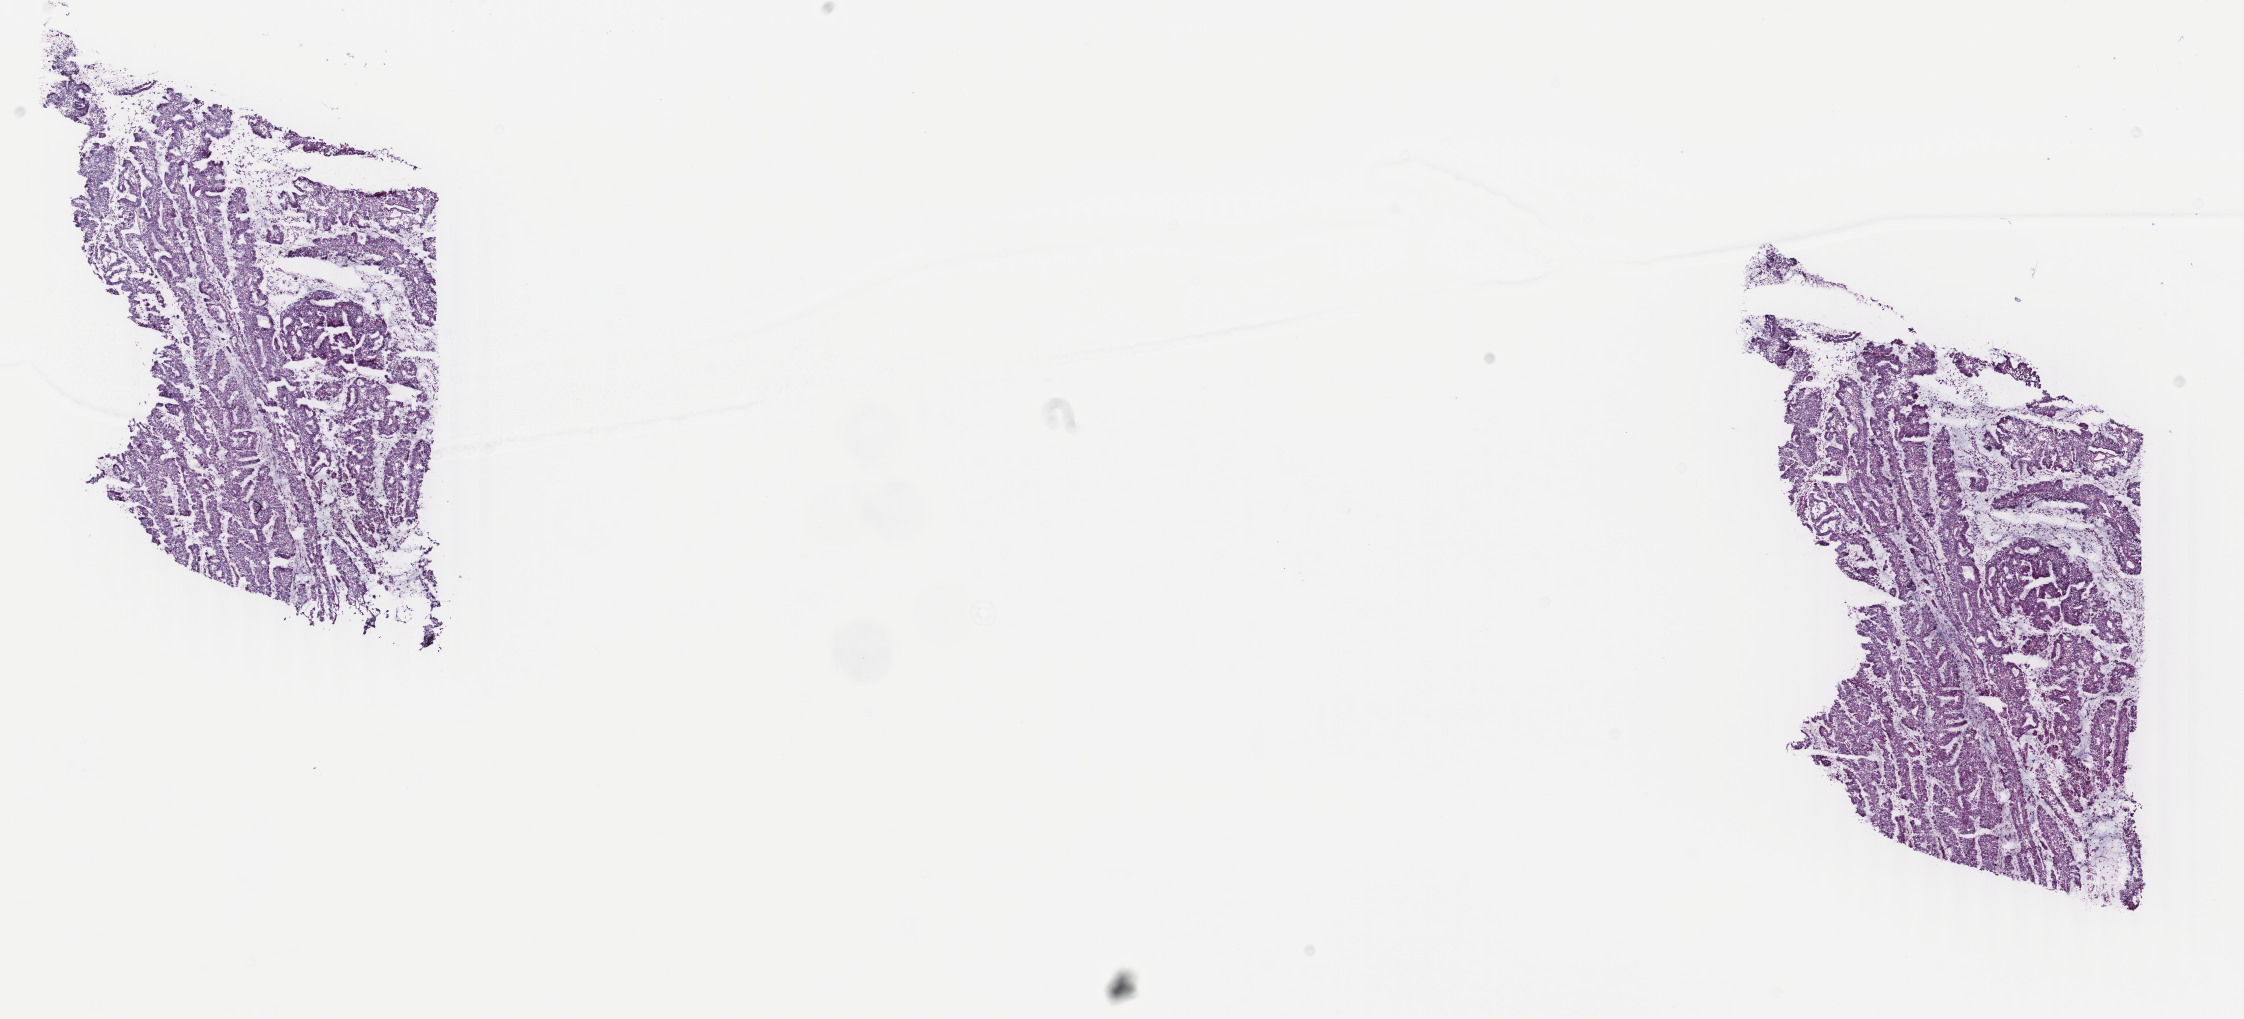
H&E-stained whole-slide image — a low-resolution overview of the entire scanned area, about 17.8 x 8.1 mm (from a 40x scan); frozen section; uterus, primary tumour sample. Female, age 53 years at initial diagnosis. Histologic grade: G1 (well differentiated). Pathologist review of this section (percent, as recorded): tumour cells 70%, tumour nuclei 70%, normal cells 0%, stromal cells 20%, necrosis 10%. Infiltration values recorded for this section: lymphocyte infiltration 40%, monocyte infiltration 20%, neutrophil infiltration 20%.
FIGO stage: IA. Diagnosis: Endometrioid adenocarcinoma, NOS (endometrium).